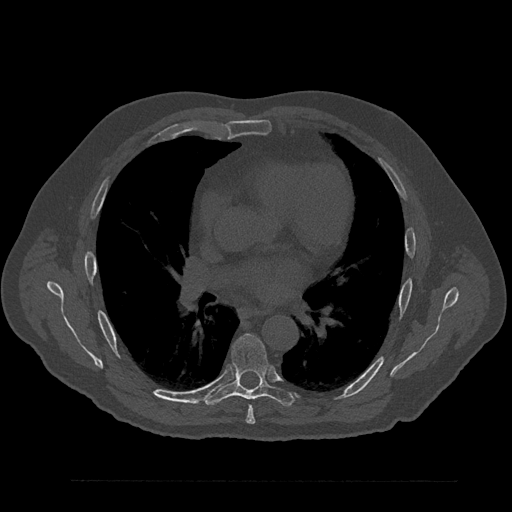
CT including the spine, one axial slice. Position 518 of 797 along the scan axis. Reconstruction kernel Br40s/3. Bone window (W 1800 / L 400 HU). 0.5 mm slice thickness. 512 × 512 image matrix, field of view 430 × 430 mm. Patient: male, 61 years. Case-level facts recorded for this patient, not image findings: primary cancer: prostate.
Structures marked on this image (semi-automatic segmentation, software-assisted and operator-edited):
- T6 vertebra: bounding box (x1, y1, x2, y2) in pixels: (246, 406, 256, 424)
- T7 vertebra: (204, 335, 294, 406)